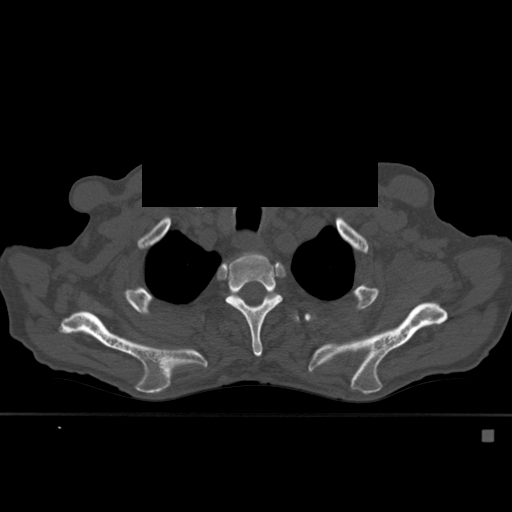
CT including the spine, one axial slice. Position 431 of 527 along the scan axis. Bone window (W 1800 / L 400 HU). 512 × 512 image matrix, field of view 373 × 373 mm. Patient: male, 78 years. From the clinical record (not read from this slice): primary cancer: prostate.
Outlined on this slice (semi-automatically segmented with operator editing):
- T2 vertebra: bounding box <239,253,260,259> (left, top, right, bottom; pixels)
- T3 vertebra: <225,254,283,357>
- T4 vertebra: <236,292,300,323>